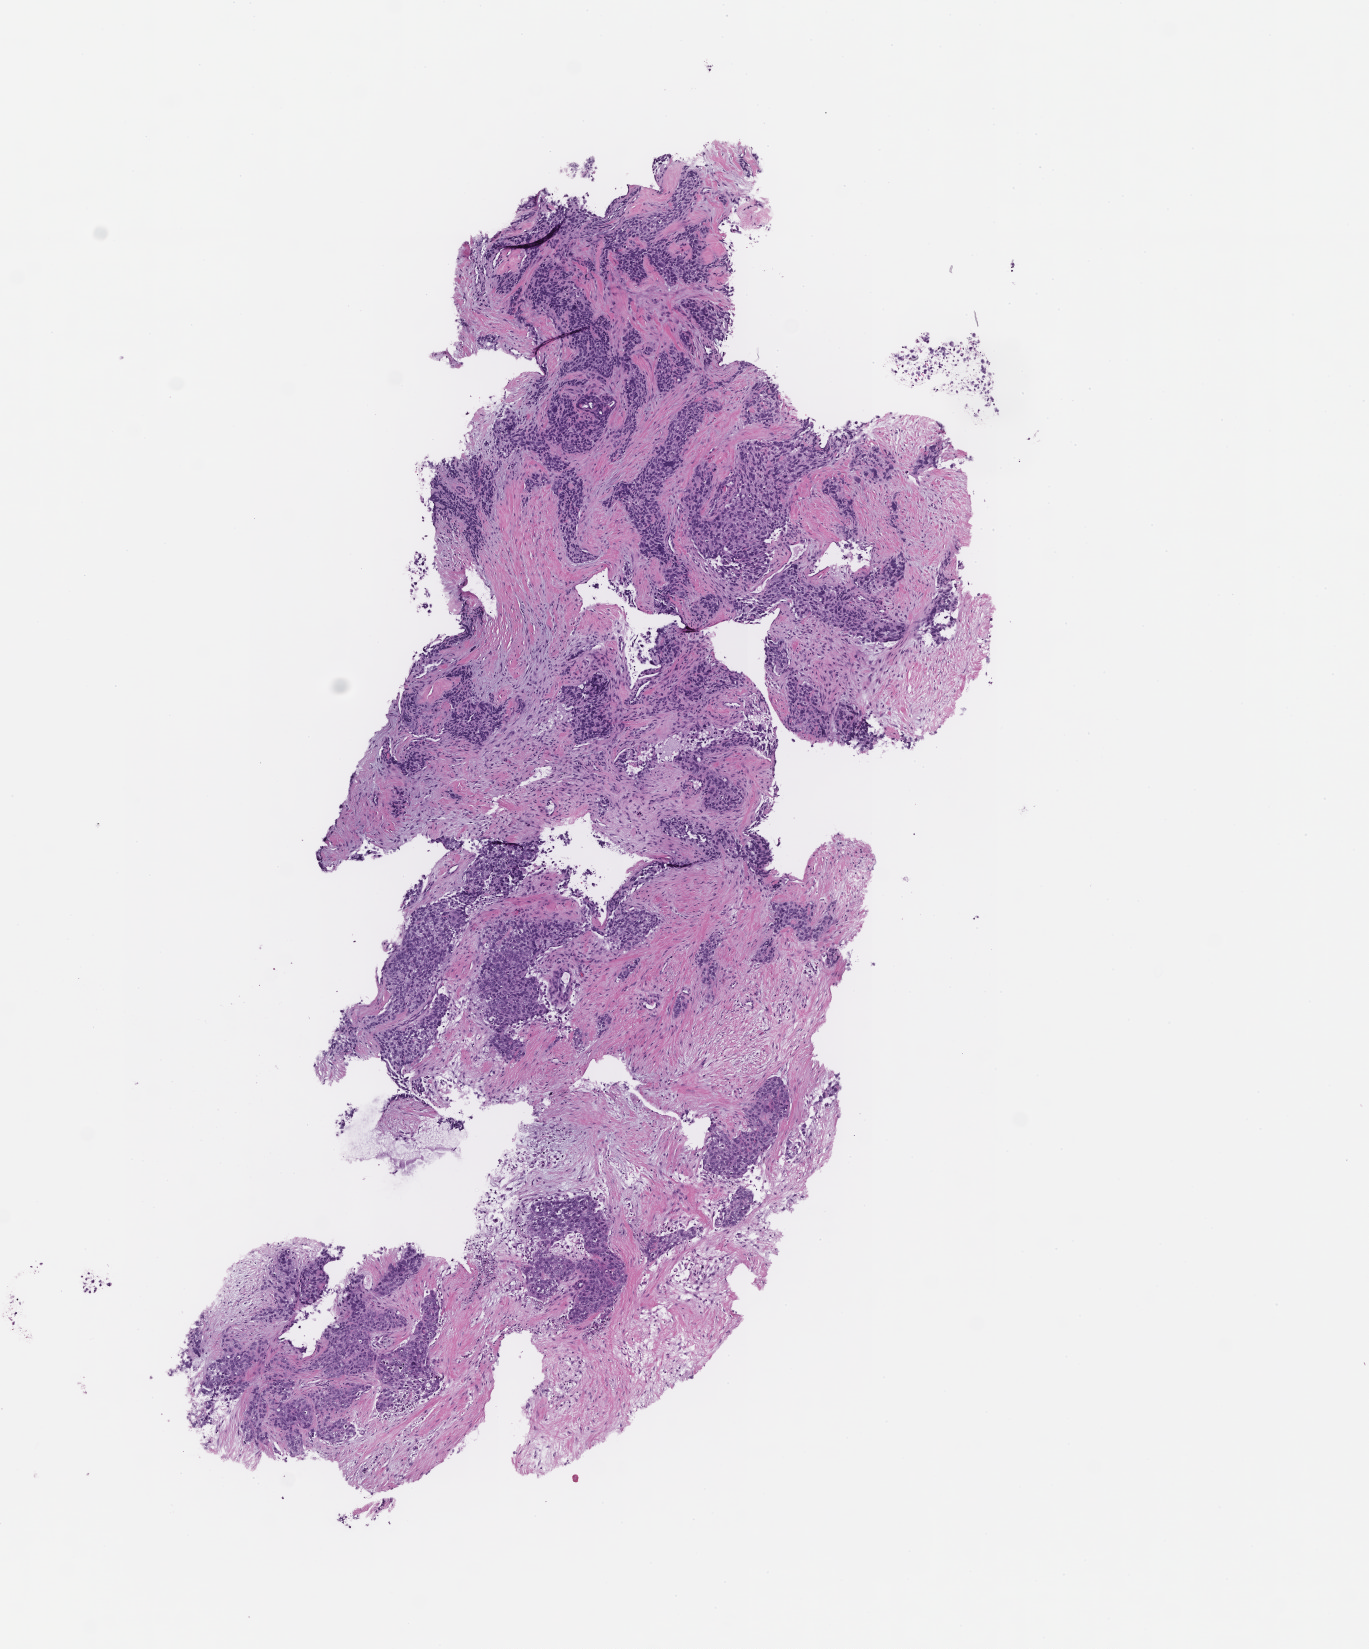
Whole-slide image, H&E stain — a low-resolution overview of the entire scanned area, about 5.5 x 6.7 mm; formalin-fixed, paraffin-embedded (FFPE) tissue; tissue site: breast; specimen time point: collected at baseline (before treatment). Patient sex: female.
This section: primary tumour tissue. Diagnosis: Invasive Breast Carcinoma.